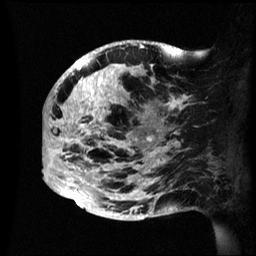
Breast MRI (dynamic contrast-enhanced), one sagittal slice. Position 22 of 60 along the scan axis. Dynamic contrast-enhanced series, image 2 of 3 at this slice position (ordered by acquisition). 1.5 T. TE 4.2 ms, TR 8.4 ms. 256 × 256 image matrix, field of view 230 × 230 mm. Patient: female, 48 years.
Structures marked on this image (semi-automatic segmentation, software-assisted and operator-edited):
- analysis volume of interest (the breast-tissue region the enhancement analysis was run in; not a lesion): bounding box [x1, y1, x2, y2] px = [43, 41, 195, 221]
- tumour enhancement mask (voxels above the 70 % enhancement threshold inside the analysis volume of interest): [43, 41, 187, 205]